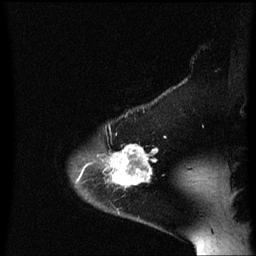
Breast MRI (dynamic contrast-enhanced), one sagittal slice; slice 51 of 60 in the series (ordered by position); dynamic contrast-enhanced series, image 2 of 3 at this slice position (ordered by acquisition); 1.5 T; TE 4.2 ms, TR 8.4 ms; 256 × 256 image matrix, field of view 200 × 200 mm. Patient: female, 54 years. From the clinical record (not read from this slice): setting: breast cancer imaged before/during neoadjuvant chemotherapy; receptor status: HR-positive, HER2-negative.
Outlined on this slice (semi-automatically segmented with operator editing):
- analysis volume of interest (the breast-tissue region the enhancement analysis was run in; not a lesion): bounding box (x1, y1, x2, y2) in pixels: (102, 134, 161, 197)
- tumour enhancement mask (voxels above the 70 % enhancement threshold inside the analysis volume of interest): (104, 144, 157, 187)